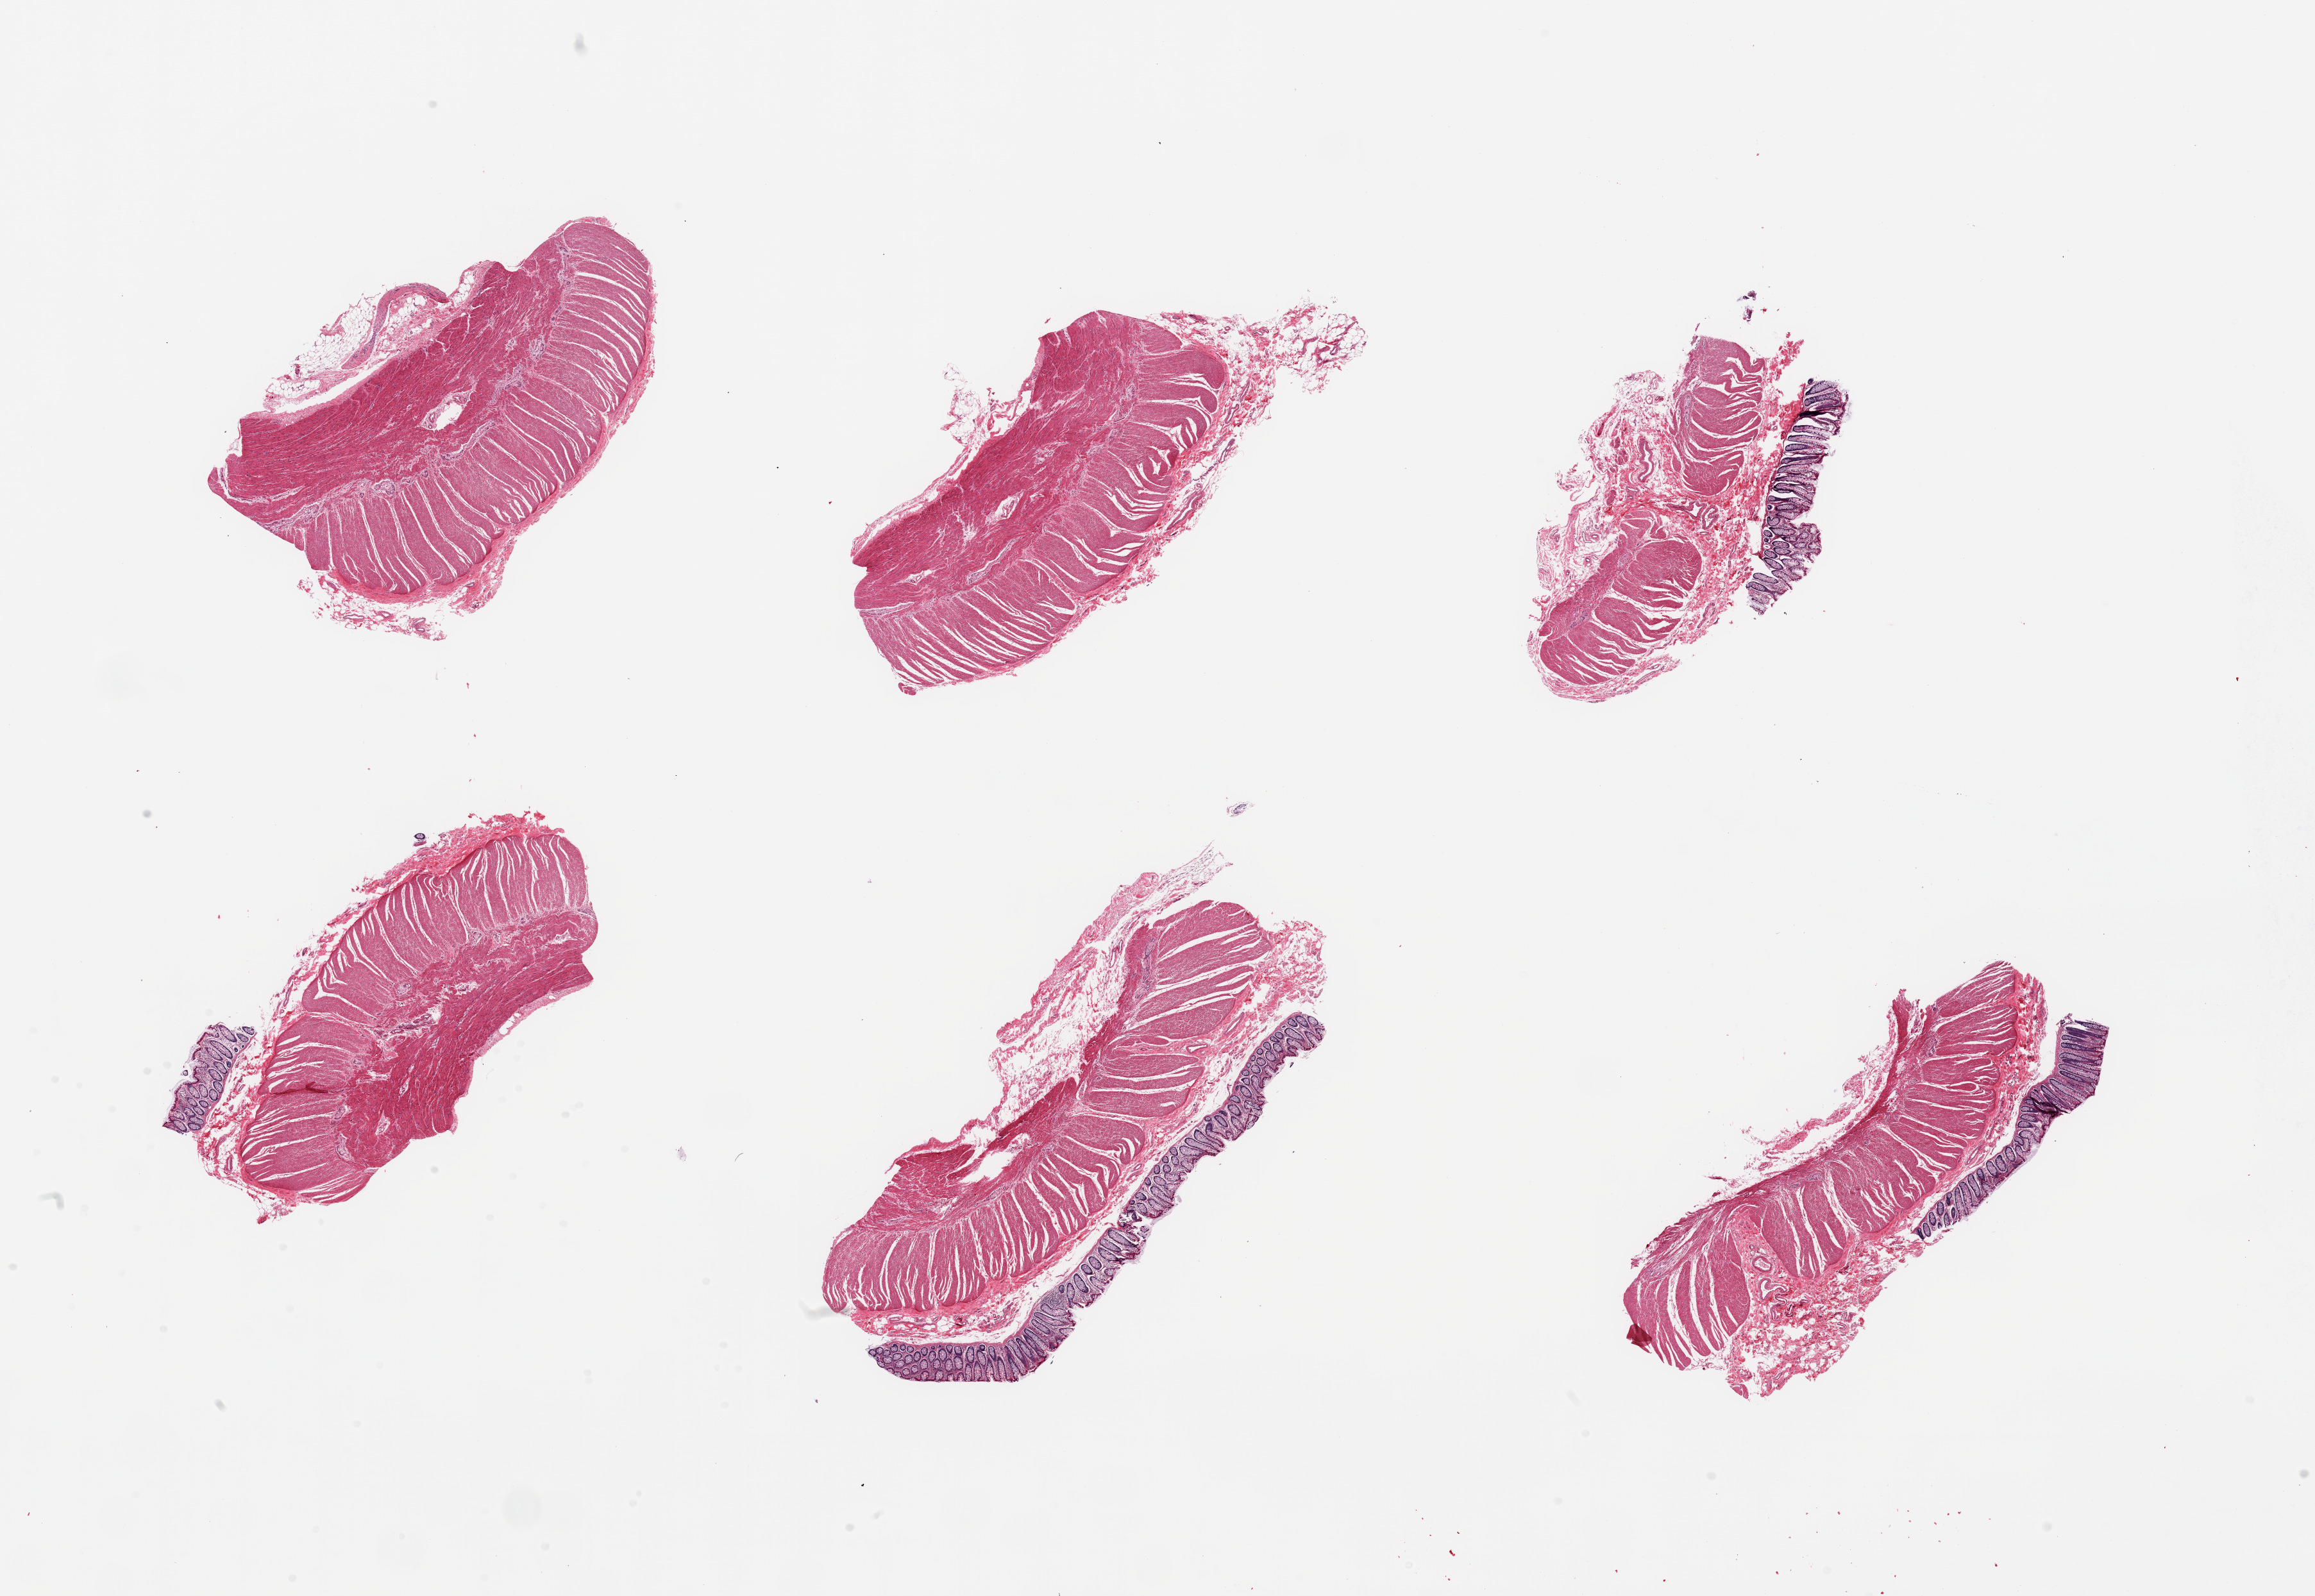
Digitized hematoxylin and eosin (H&E)-stained section — a low-resolution overview of the entire scanned area, about 28.5 x 19.7 mm, PAXgene-fixed paraffin-embedded (PFPE) section, sampled site (target tissue): sigmoid colon, tissue donor sample. Donor: male.
- reviewer comment on this tissue sample: 6 pieces; muscularis, 4 of 6 include strips of mucosa